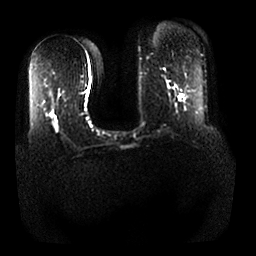
Breast MRI, one axial slice; position 13 of 25 along the scan axis; diffusion-weighted series; image 2 of 4 stored at this slice position (different b-values; order by instance number); 1.5 T; 4 mm slice thickness; 256 × 256 image matrix, field of view 380 × 380 mm. Female patient.
Outlined on this slice (expert manual segmentation):
- tumour on diffusion-weighted imaging: bounding box <54,116,58,131> (left, top, right, bottom; pixels)